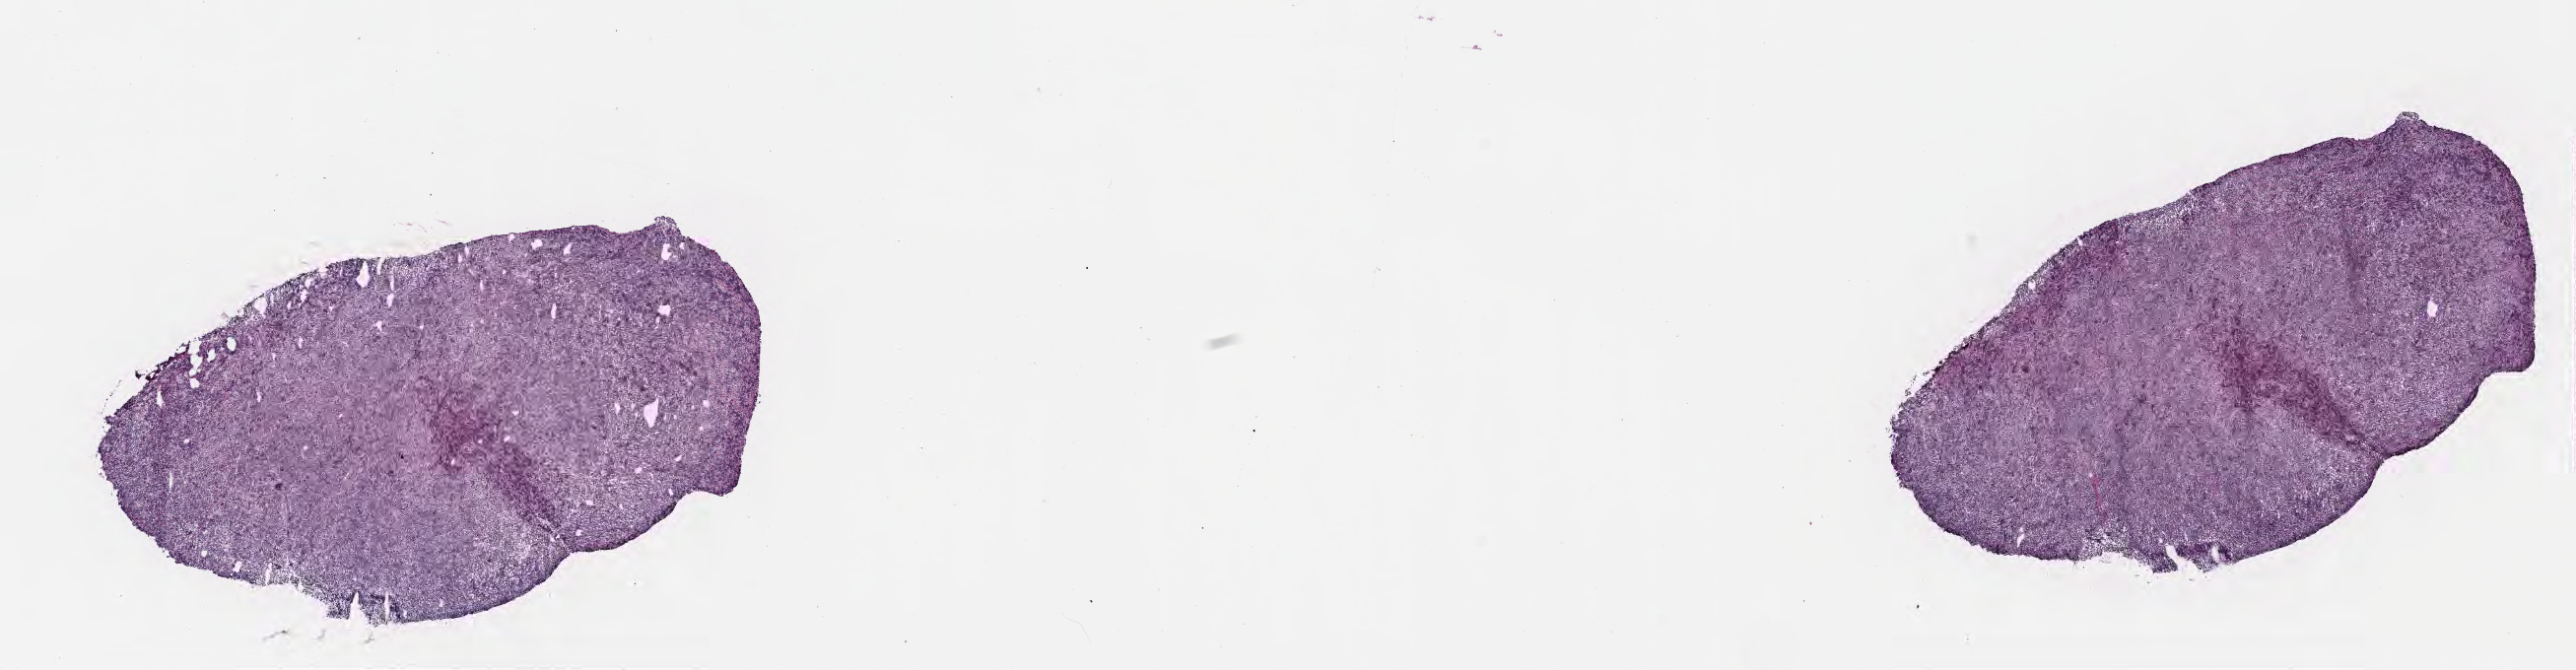
Haematoxylin and eosin whole-slide image — low-resolution overview of the scanned area, about 21.1 x 5.5 mm; cryosection; specimen: primary tumor; anatomic site: buccal mucosa. Male patient; age at initial diagnosis 5 years. Pathologist review of this section (percent, as recorded): tumor cells 90%, tumor nuclei 90%, stromal cells 5%, necrosis 5%, normal cells 0%. Inflammatory infiltration, as recorded: lymphocyte infiltration 50%, monocyte infiltration 30%, neutrophil infiltration 5%.
- Ann Arbor stage (patient): Stage II
- histologic diagnosis: Diffuse large B-cell lymphoma, NOS